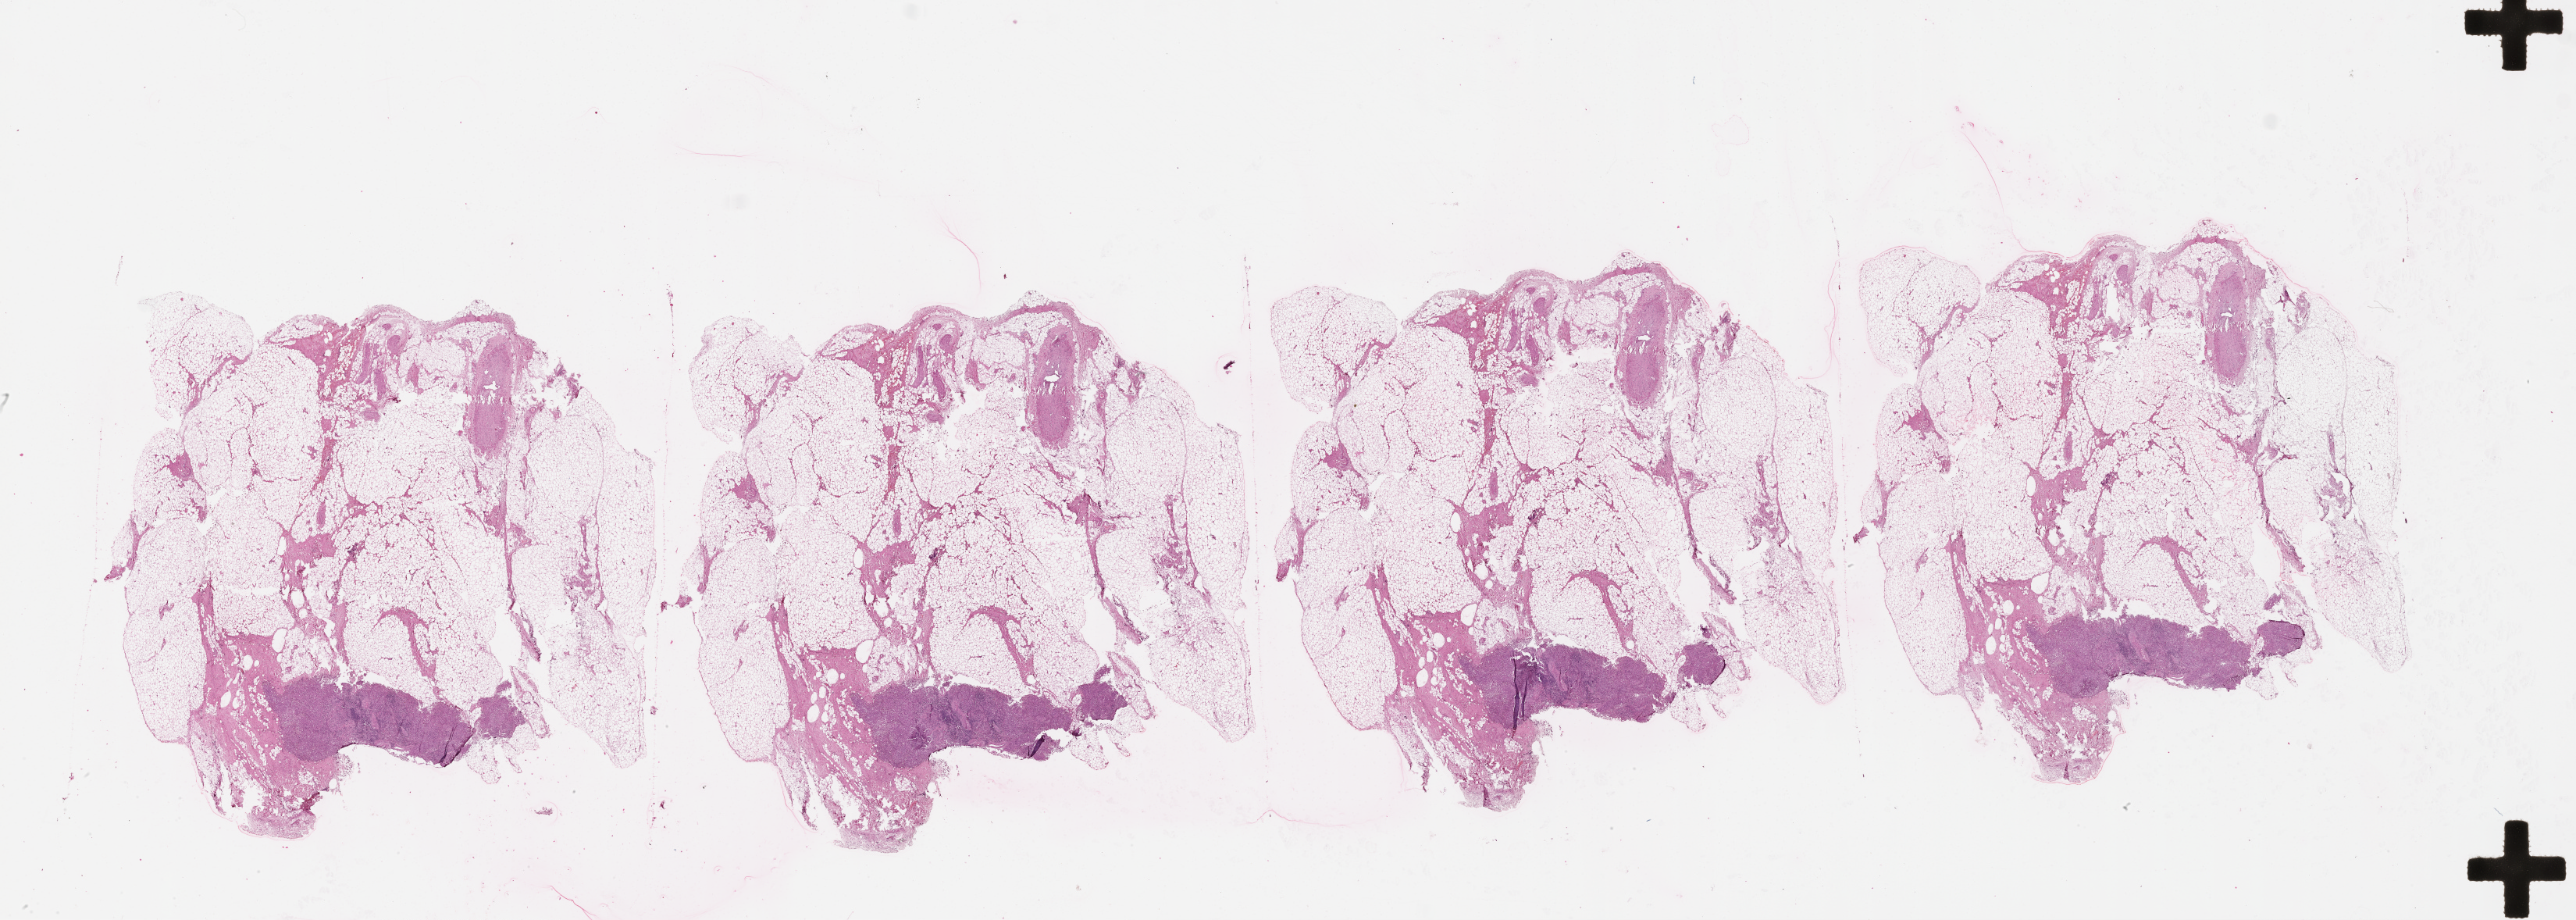
Digitized H&E tissue section (whole slide) — a low-resolution overview of the entire scanned area, about 53.1 x 19.0 mm. Patient: male, age 87 years.
* patient diagnosis: Malignant melanoma, NOS